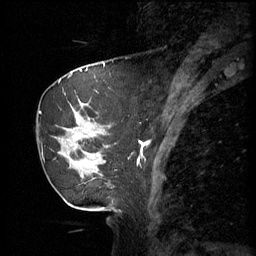
Breast MRI (dynamic contrast-enhanced), one sagittal slice; slice 18 of 60 in the series (ordered by position); 3 images stored at this slice position (order not interpretable as contrast timing); 1.5 T; TE 4.2 ms, TR 11 ms; 2 mm slice thickness; 256 × 256 image matrix, field of view 220 × 220 mm. Patient: female, 69 years.
Structures marked on this image (semi-automatically segmented with operator editing):
- analysis volume of interest (the breast-tissue region the enhancement analysis was run in; not a lesion): bounding box (x1, y1, x2, y2) in pixels: (39, 88, 115, 189)
- tumour enhancement mask (voxels above the 70 % enhancement threshold inside the analysis volume of interest): (67, 102, 103, 165)